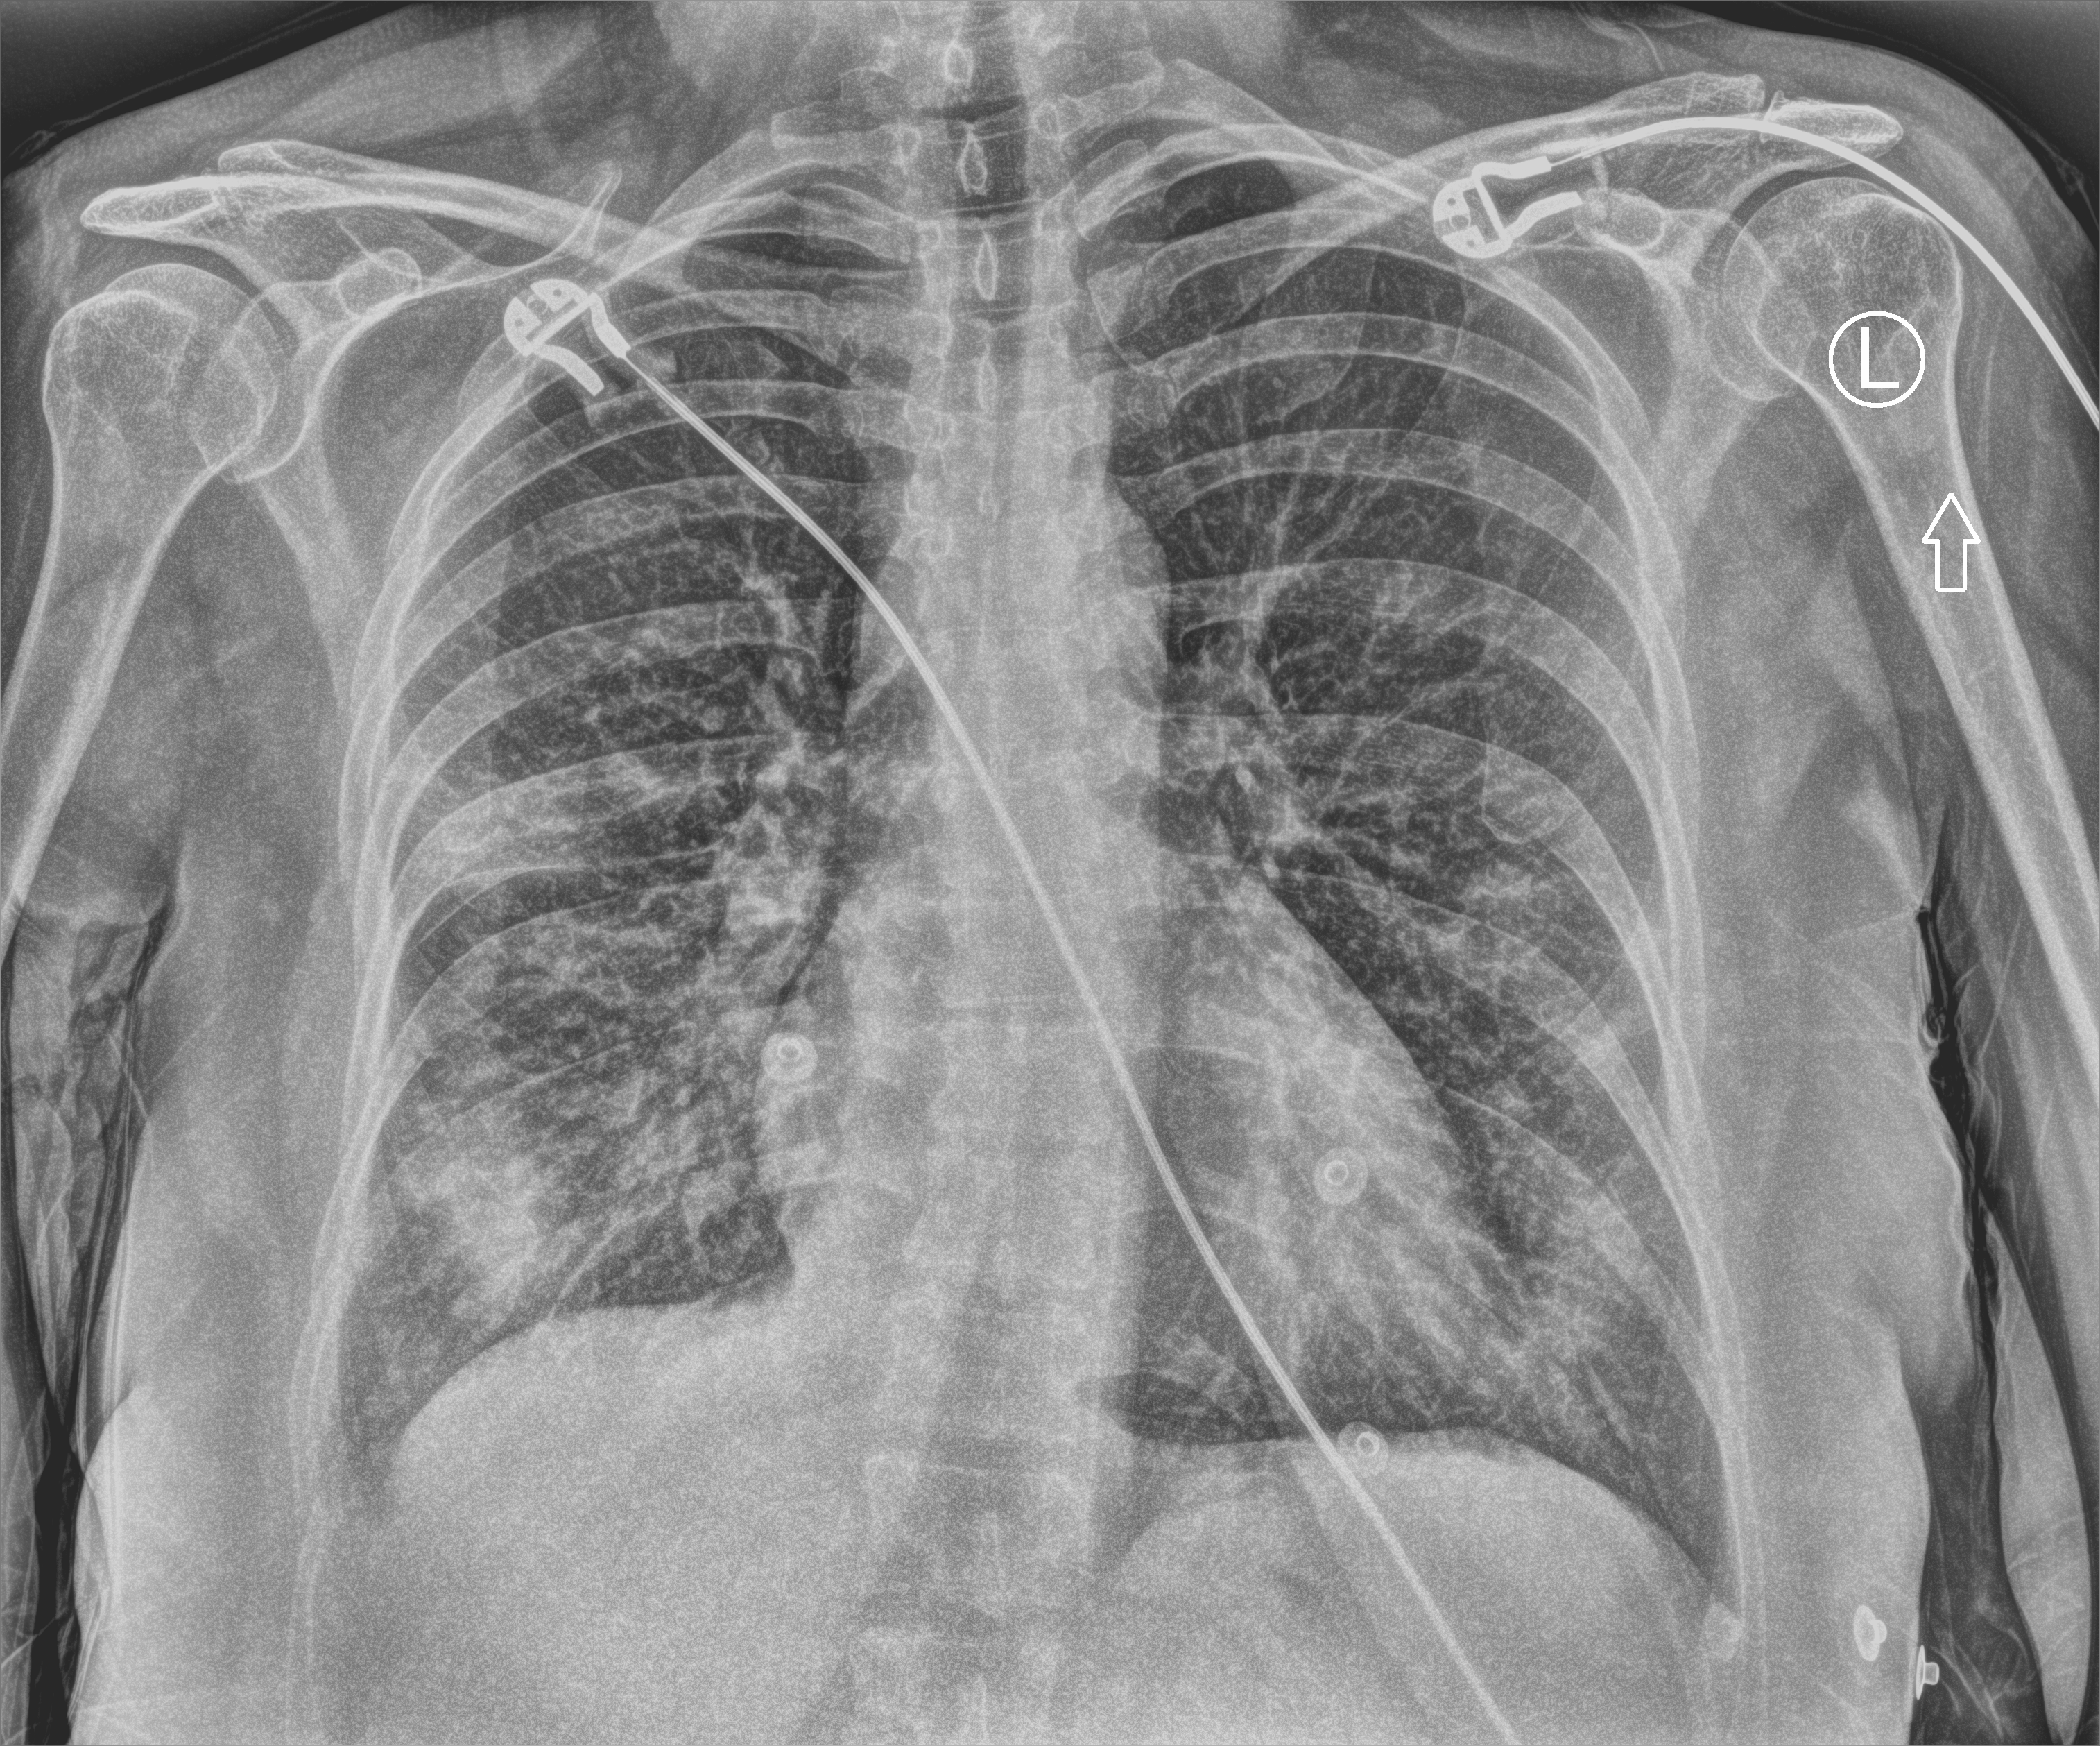
Portable chest radiograph; anteroposterior (AP) projection. Female patient hospitalised with COVID-19, age 18–59 years.
Hospital-stay facts (about this admission, not read from this image; timing relative to this image not recorded): length of hospital stay: 1 day.